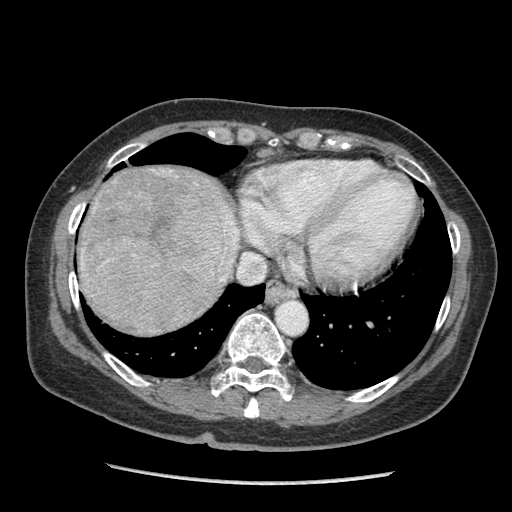
Contrast-enhanced abdominal CT (liver protocol), one axial slice. Slice 84 of 105 in the series (ordered by position). 140 kVp. Soft-tissue window (W 400 / L 40 HU). 2.5 mm slice thickness. 512 × 512 image matrix, field of view 340 × 340 mm. From the clinical record (not read from this slice): diagnosis: hepatocellular carcinoma (patient treated with transarterial chemoembolisation; whether this scan precedes or follows treatment is not stated here); TNM stage (as recorded): Stage-I; Child-Pugh class: A; tumour differentiation: moderately differentiated; tumour nodularity: uninodular.
Outlined on this slice (semi-automatic segmentation, software-assisted and operator-edited):
- liver parenchyma outside the tumour (the mass and vessels are separate outlines, so this box may not span the whole liver): bounding box [x1, y1, x2, y2] px = [78, 166, 240, 322]
- mass: [80, 168, 235, 336]
- liver vessels: [222, 228, 238, 280]